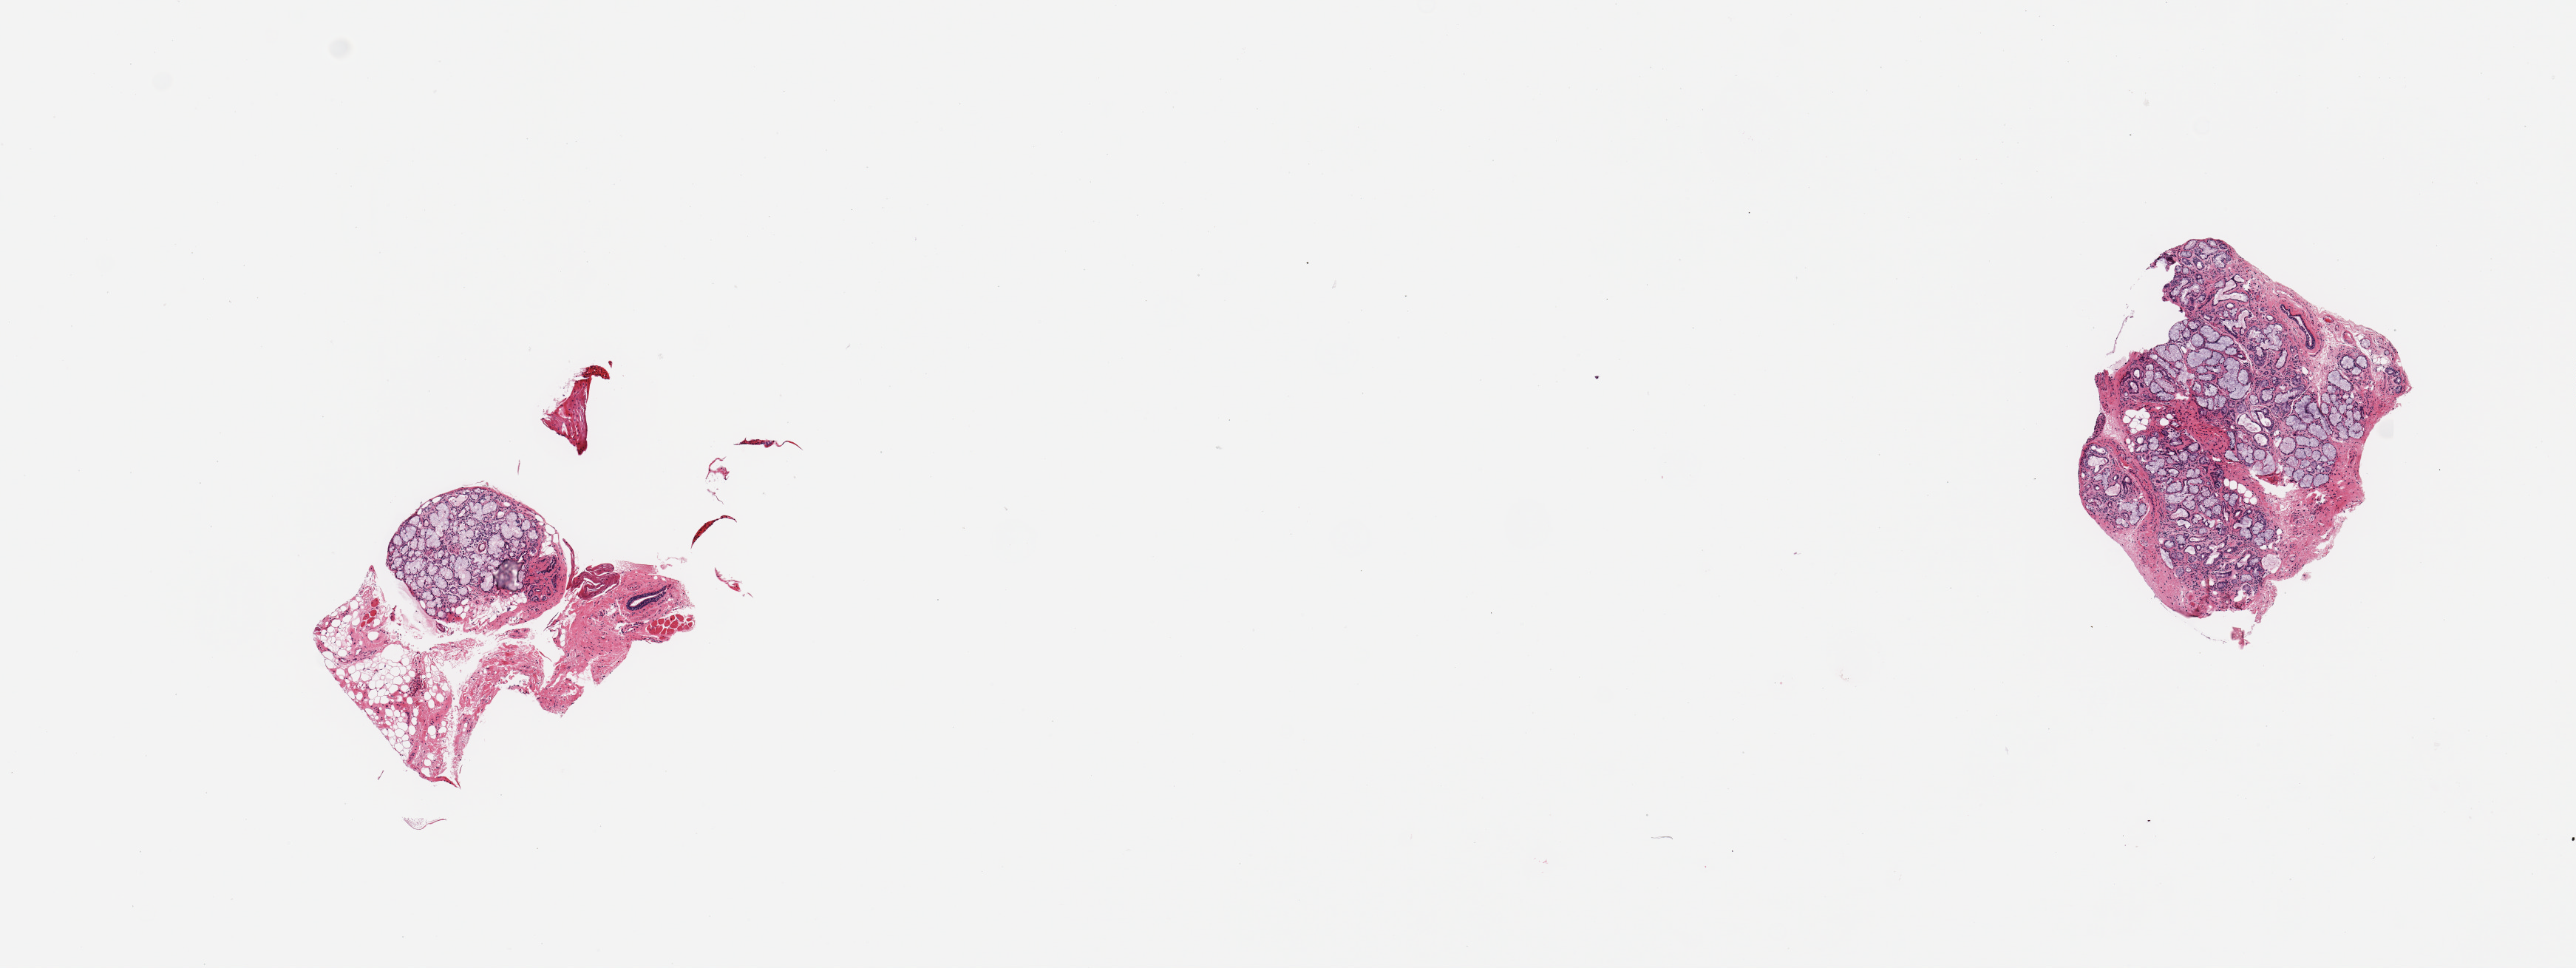
Haematoxylin and eosin whole-slide image, a low-resolution overview of the entire scanned area, about 13.8 x 5.2 mm, PAXgene-fixed, paraffin-embedded tissue, target tissue: minor salivary gland, tissue donor sample.
- pathologist's review note for this sample: 2 pieces; 1 piece is all salivary gland; other is 50% gland with remainder fibroadipose and muscle tissue